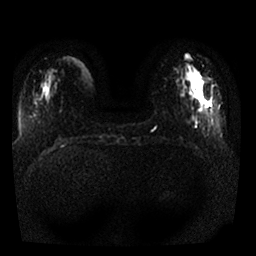
Breast MRI, one axial slice. Slice 6 of 25 in the series (ordered by position). Diffusion-weighted series; image 2 of 4 stored at this slice position (different b-values; order by instance number). 1.5 T. 4 mm slice thickness. 256 × 256 image matrix. Female patient.
Structures marked on this image (outlined manually by an expert reader):
- tumour on diffusion-weighted imaging: bounding box (x1, y1, x2, y2) in pixels: (204, 102, 210, 107)